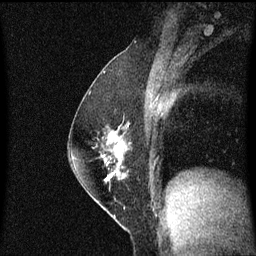
Breast MRI (dynamic contrast-enhanced), one sagittal slice. Position 33 of 60 along the scan axis. Dynamic contrast-enhanced series, image 2 of 3 at this slice position (ordered by acquisition). 1.5 T. TE 4.2 ms, TR 8.4 ms. 2 mm slice thickness. 256 × 256 image matrix. Patient: female, 52 years. From the clinical record (not read from this slice): setting: breast cancer imaged before/during neoadjuvant chemotherapy; receptor status: HER2-positive.
Outlined on this slice (semi-automatic segmentation, software-assisted and operator-edited):
- analysis volume of interest (the breast-tissue region the enhancement analysis was run in; not a lesion): bounding box (x1, y1, x2, y2) in pixels: (71, 118, 133, 187)
- tumour enhancement mask (voxels above the 70 % enhancement threshold inside the analysis volume of interest): (106, 132, 124, 181)